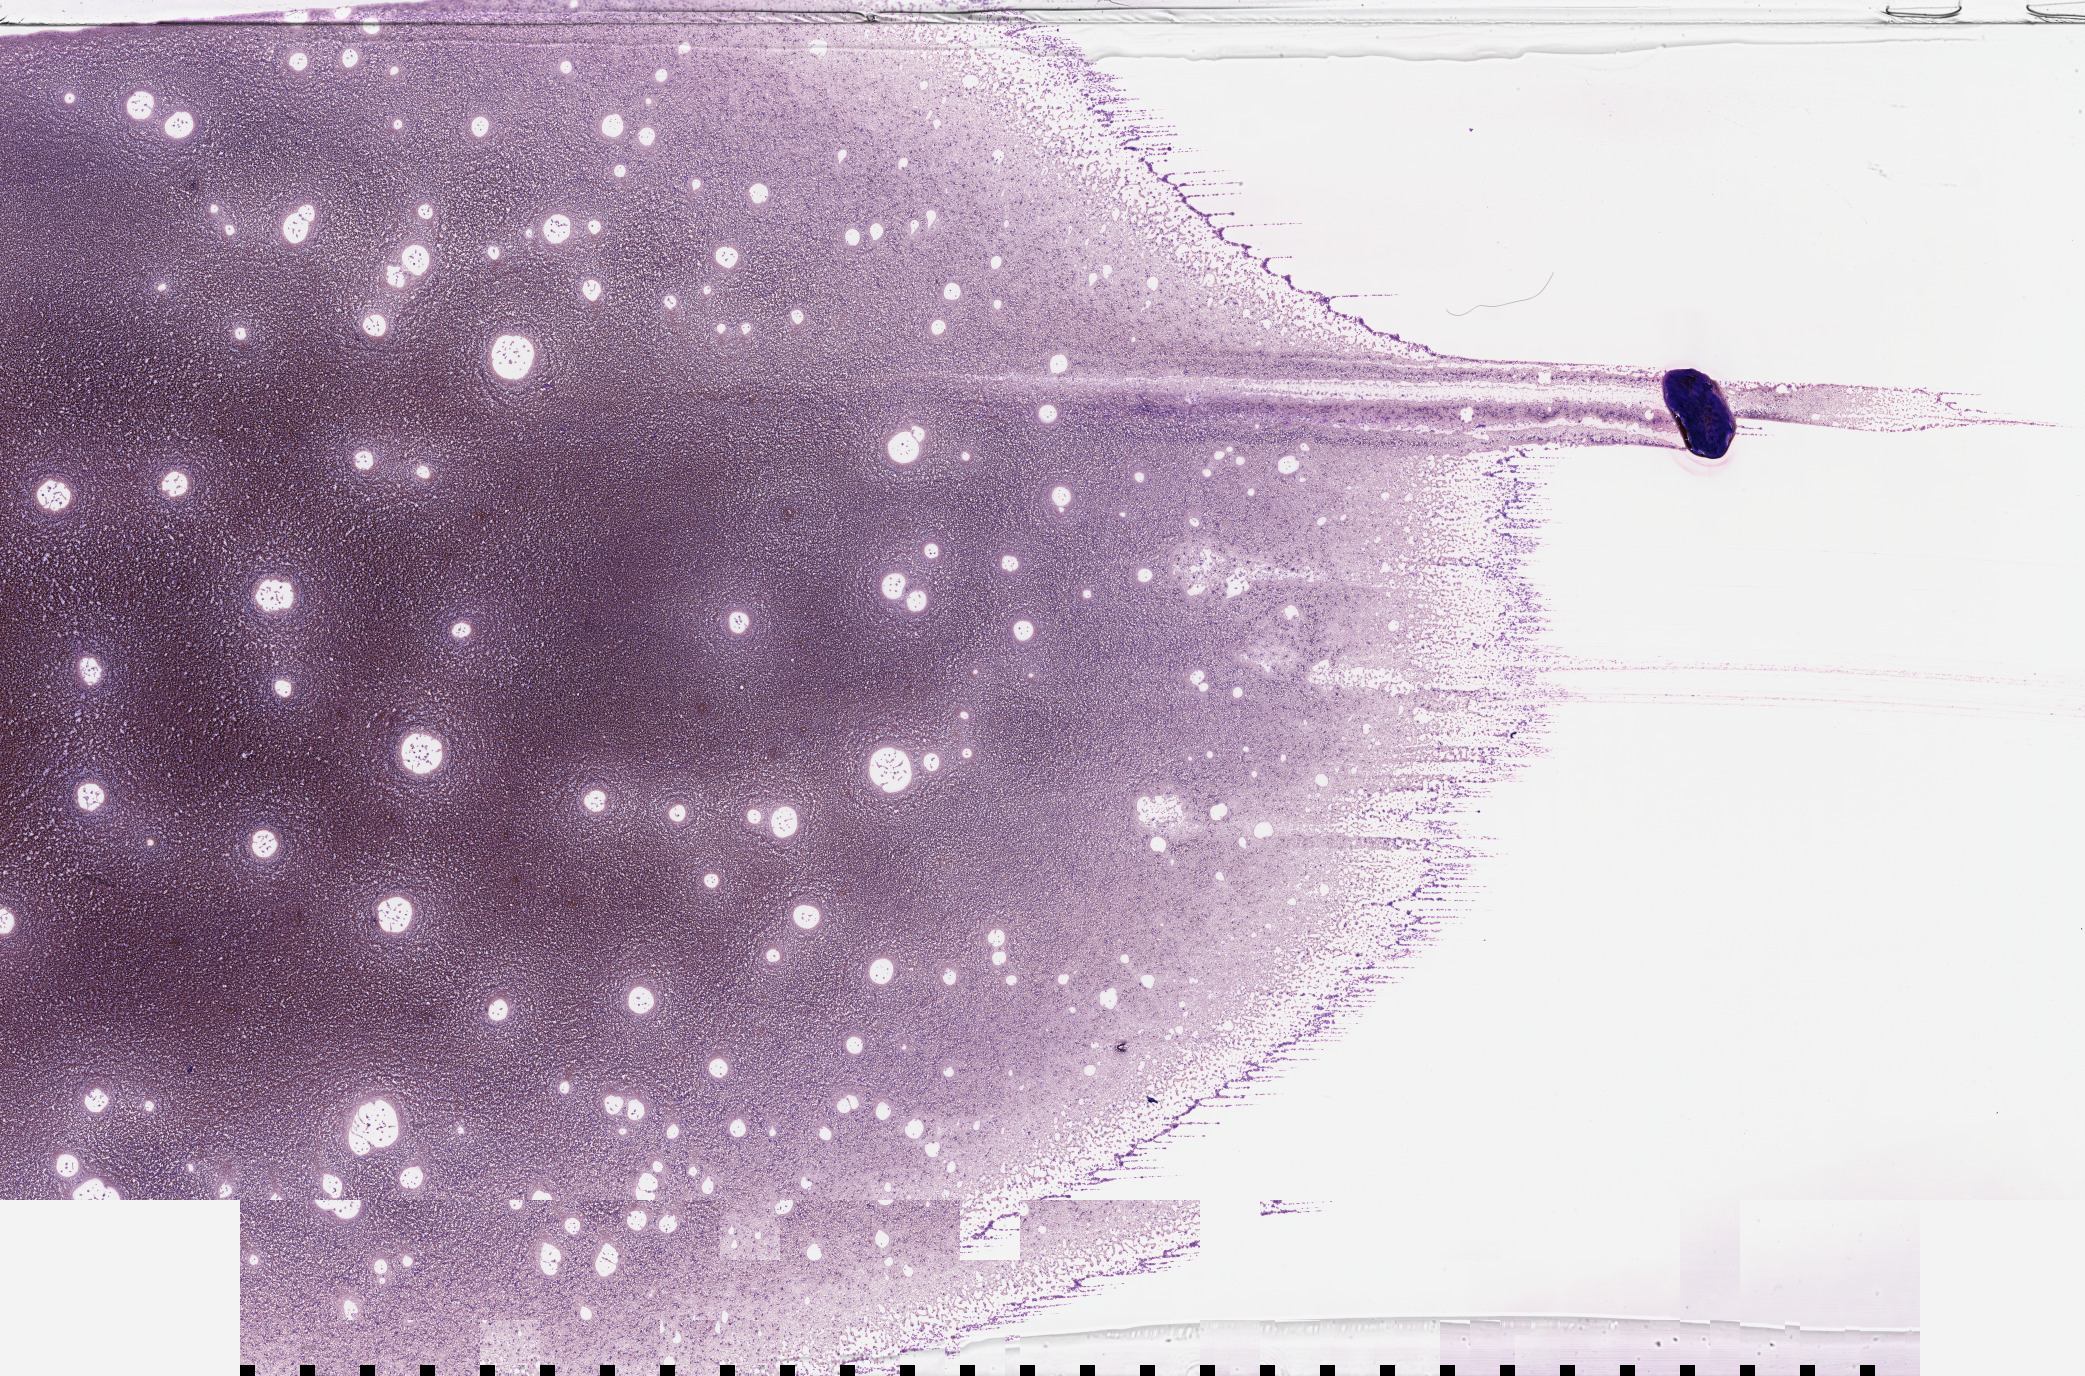
Wright–Giemsa whole-slide image, low-resolution overview of the scanned area, about 33.7 x 22.2 mm; frozen section (tissue freezing medium); specimen: primary tumor; site: bone marrow. Patient male; age 16 years. Pathologist review of this section (percent, as recorded): tumor cells 95%, tumor nuclei 95%, stromal cells 0%, necrosis 0%, normal cells 5%. Infiltration values recorded for this section: lymphocyte infiltration 10%, monocyte infiltration 30%, neutrophil infiltration 60%.
* histologic diagnosis: Burkitt lymphoma, NOS
* section: top of the tissue portion